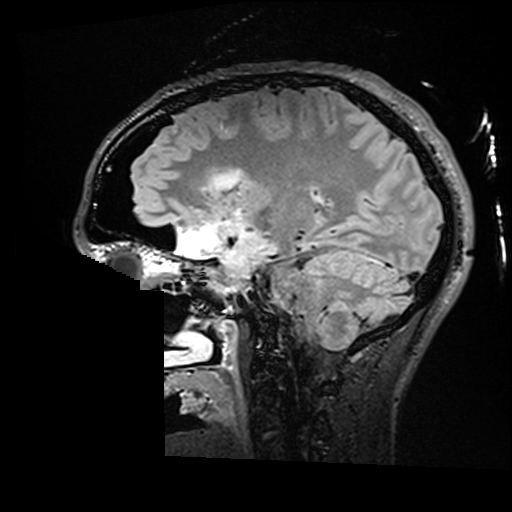
Brain MRI from a brain-tumour surgery series, one sagittal slice. Slice 102 of 176 in the series (ordered by position). T2 FLAIR. 512 × 512 image matrix. From the clinical record (not read from this slice): histopathology: Astrocytoma; WHO grade: 2; IDH mutation: yes.
Structures marked on this image (expert manual segmentation):
- residual tumour: bounding box <212,170,244,190> (left, top, right, bottom; pixels)